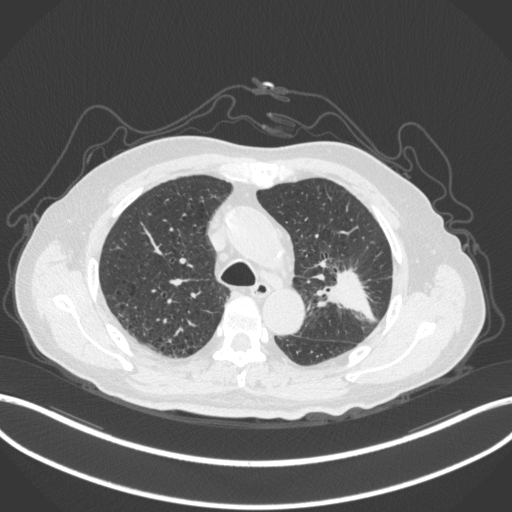
Chest CT, one axial slice; position 202 of 331 along the scan axis; 120 kVp; lung window (W 1500 / L -600 HU); 1 mm slice thickness; 512 × 512 image matrix, field of view 400 × 400 mm. Patient: male, 79 years. Case-level facts recorded for this patient, not image findings: clinical TNM (as recorded): T2a N1 M1; histopathological grade: G3.
Structures marked on this image (bounding box drawn by a radiologist):
- lung tumour (recorded histology: adenocarcinoma): box from (x=312, y=261) to (x=376, y=323) px